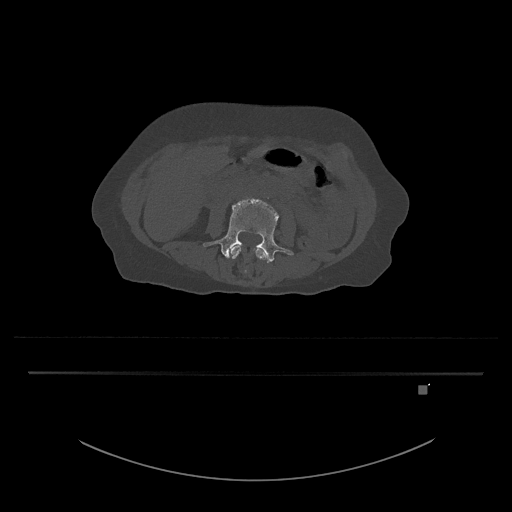
CT including the spine, one axial slice. Slice 381 of 797 in the series (ordered by position). Bone window (W 1800 / L 400 HU). 0.5 mm slice thickness. 512 × 512 image matrix, field of view 500 × 500 mm. Patient: female, 57 years. From the clinical record (not read from this slice): primary cancer: cervical.
Annotated regions visible in this slice (semi-automatic segmentation, software-assisted and operator-edited):
- L3 vertebra: bounding box (x1, y1, x2, y2) in pixels: (230, 245, 267, 273)
- L4 vertebra: (203, 198, 294, 263)